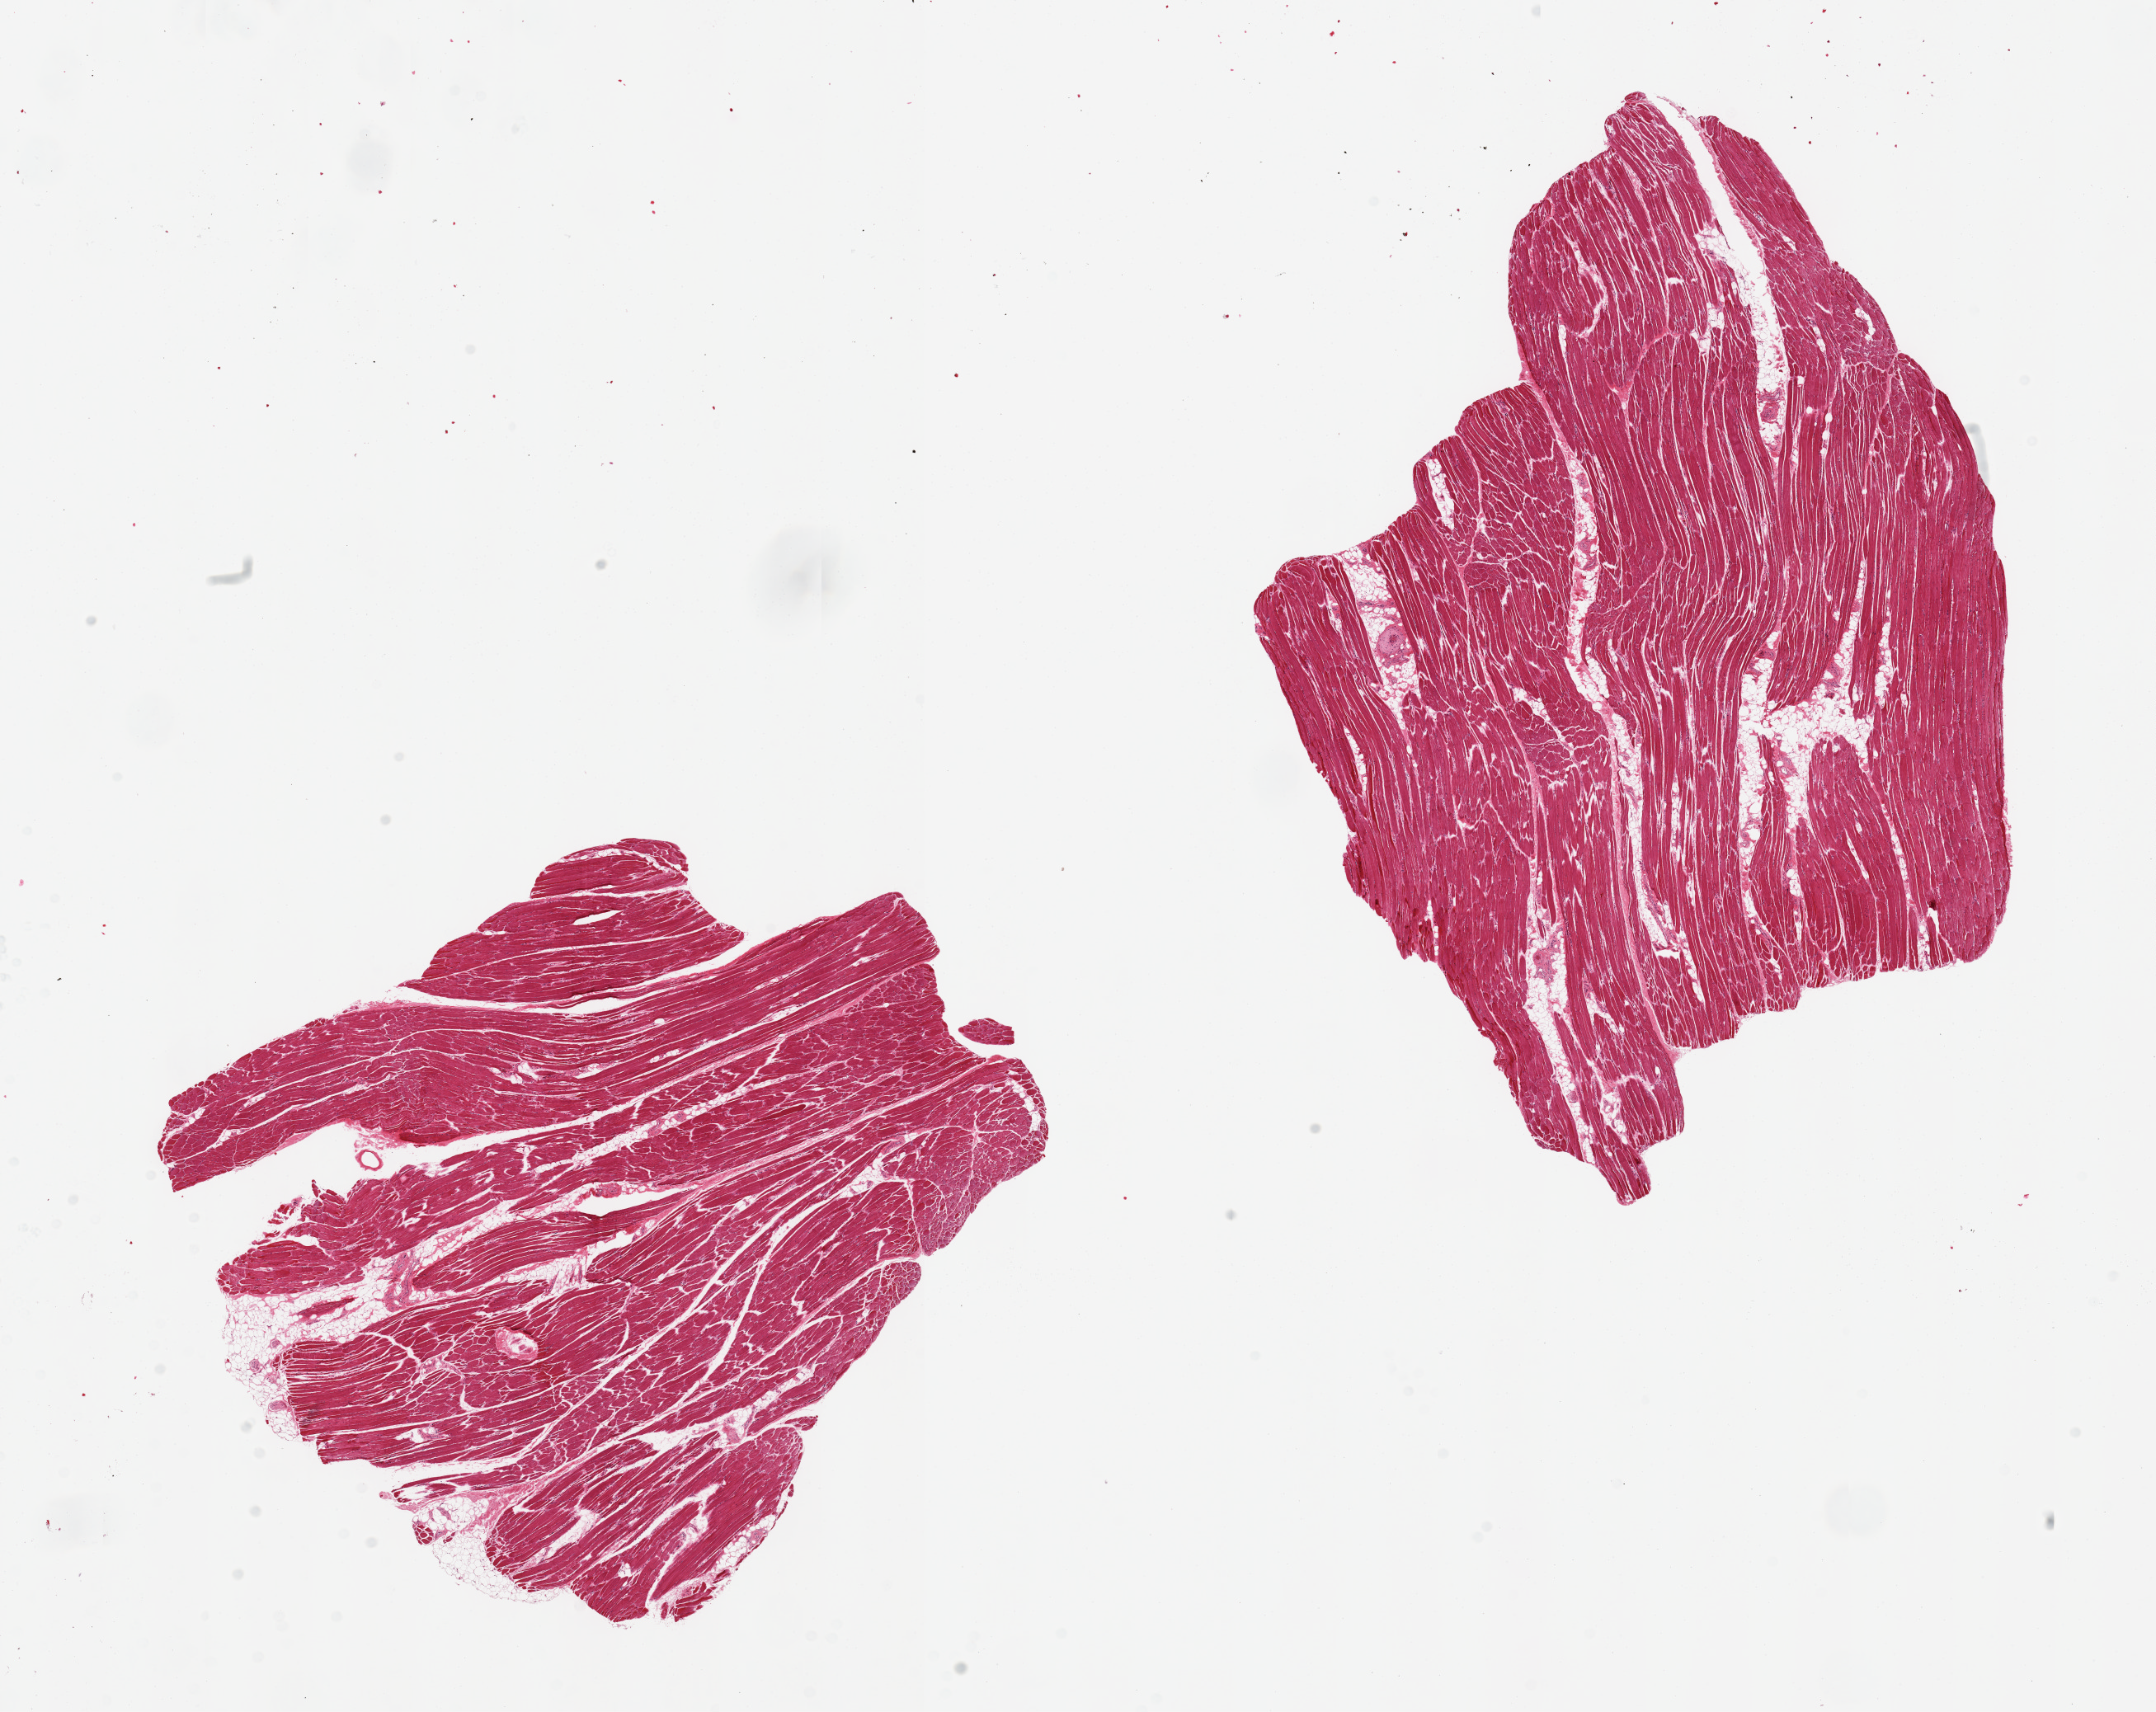
Haematoxylin and eosin whole-slide image — a low-resolution overview of the entire scanned area, about 20.7 x 16.4 mm. PAXgene-fixed, paraffin-embedded tissue. Target tissue: skeletal muscle. Tissue donor sample. Donor sex: female.
• reviewer comment on this tissue sample: 2 pieces, ~10% interstitial fat